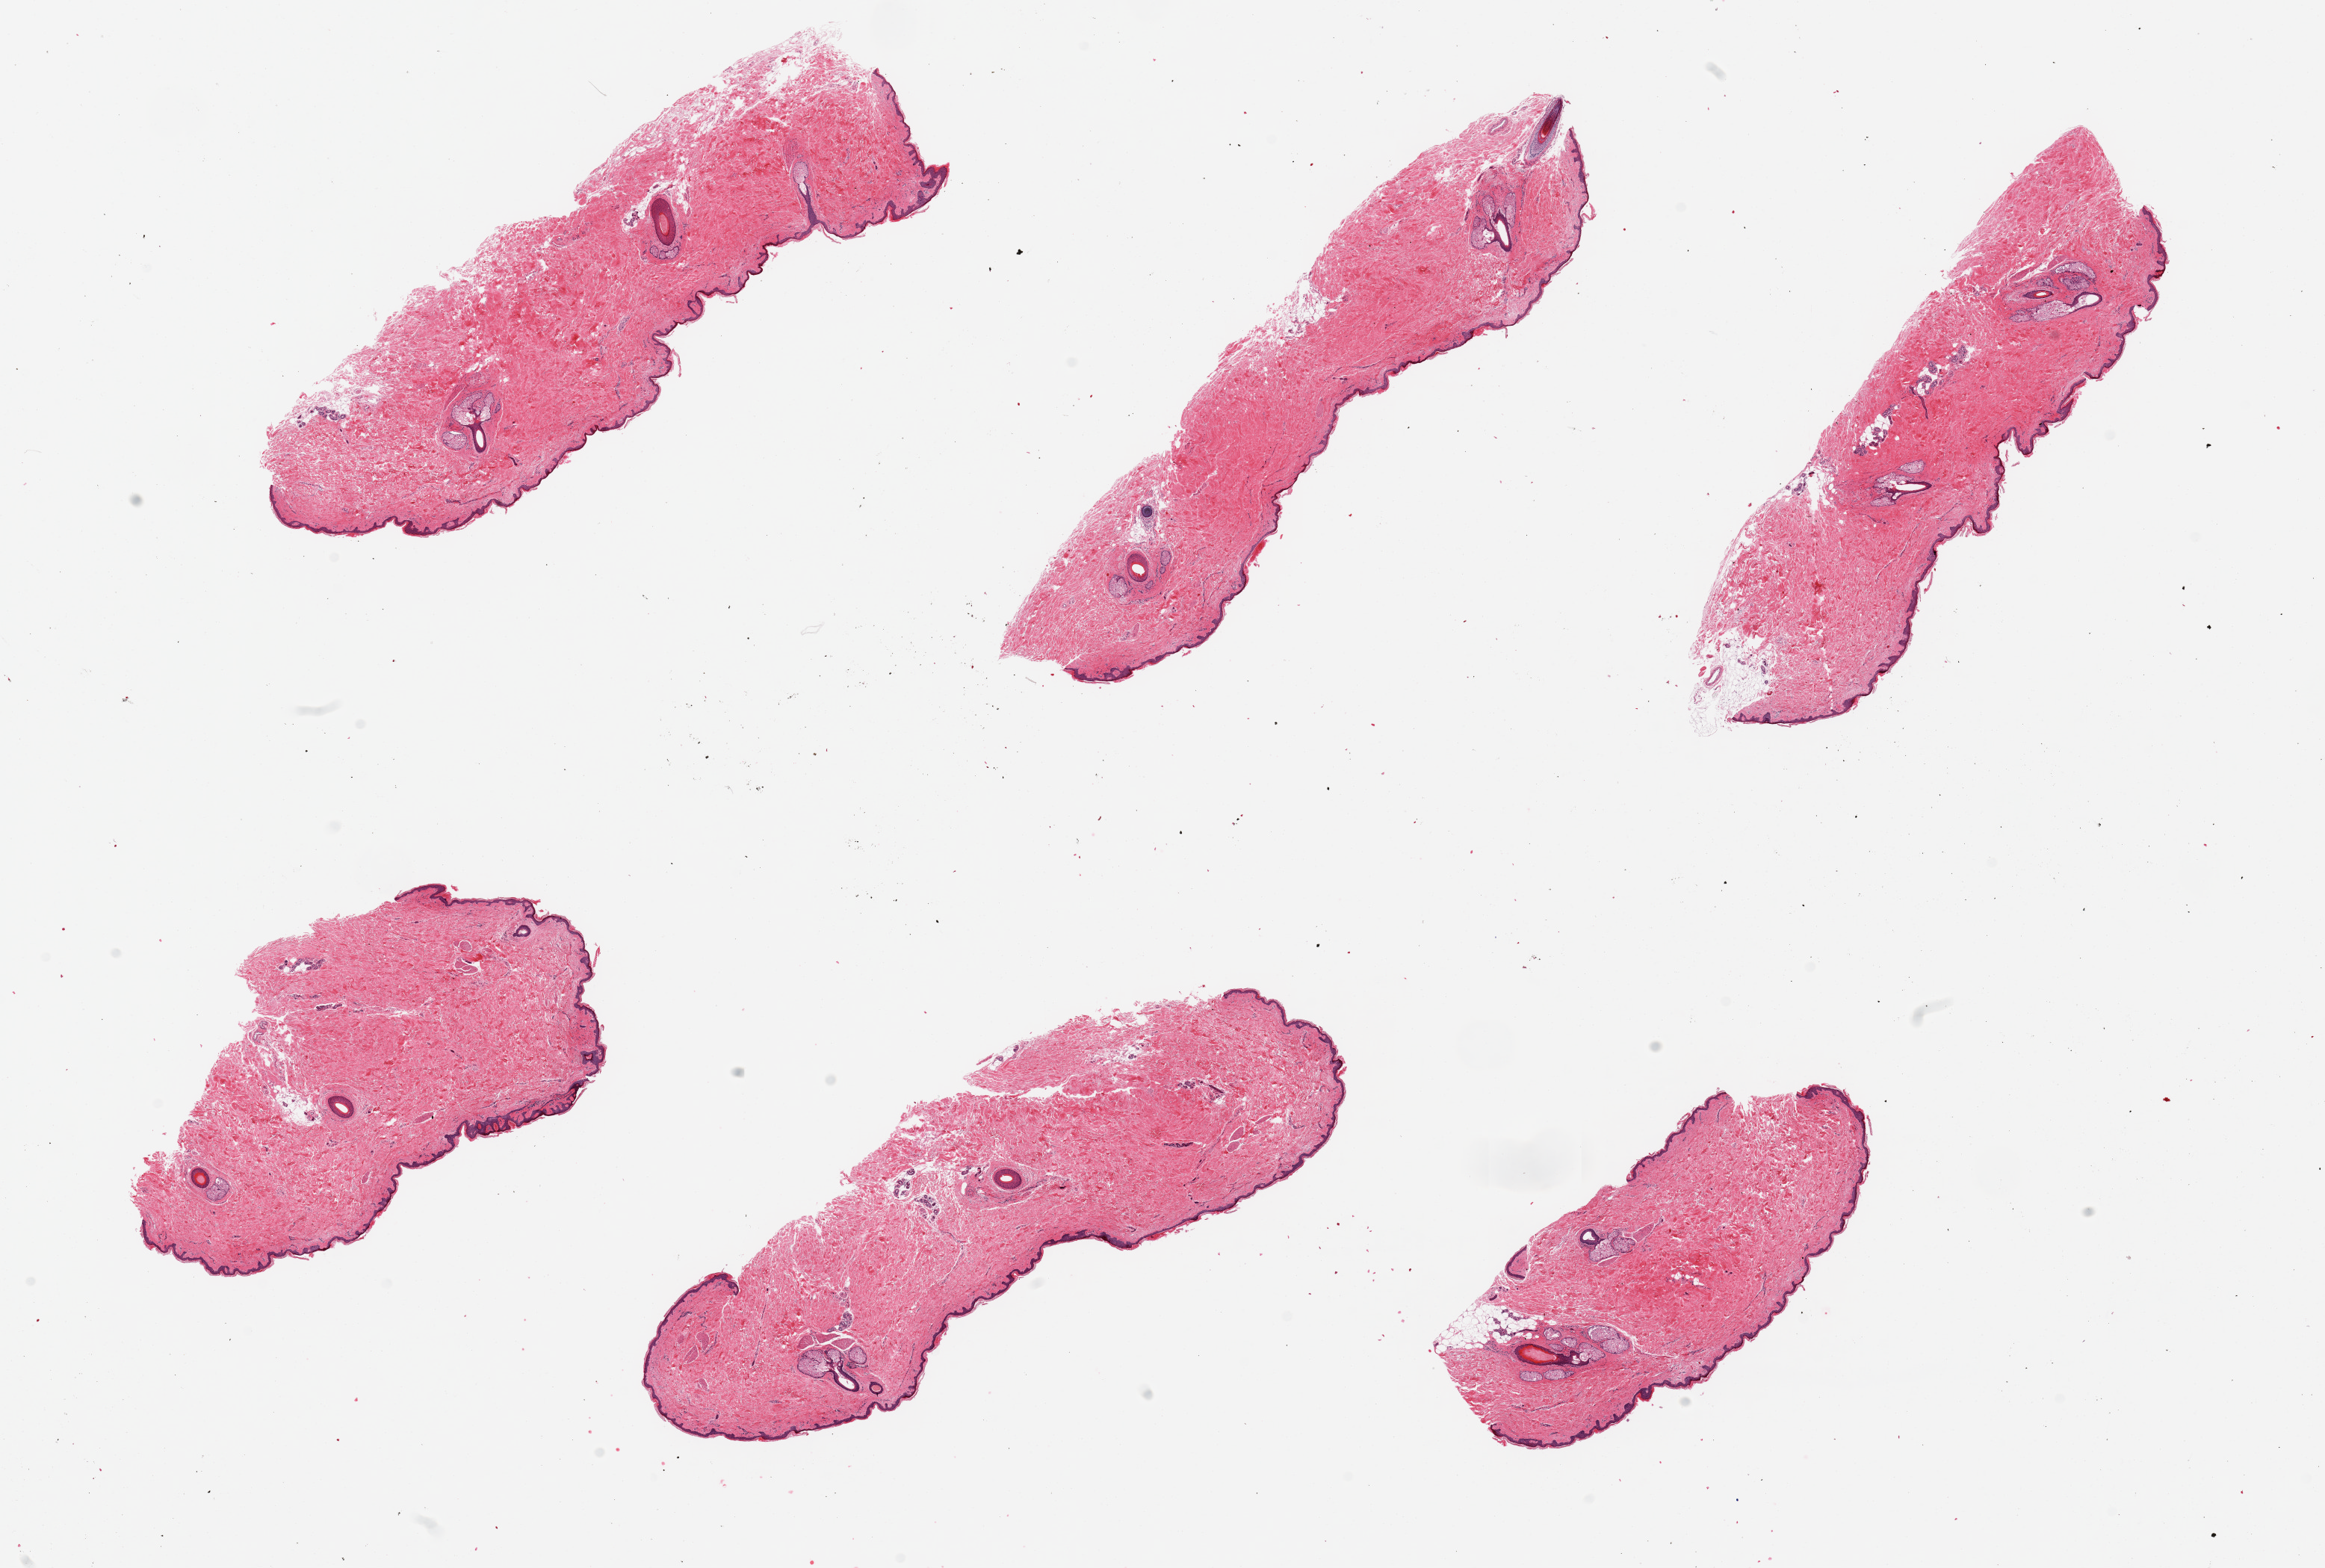
Digitized H&E-stained section, shown as a low-resolution overview of the whole scanned area (about 24.6 x 16.6 mm, slide scanned at 20x). PAXgene-fixed paraffin-embedded (PFPE) section. Target tissue: skin of suprapubic region. Donor tissue sample.
Pathologist's review note for this sample: 6 pieces; at least 2 hair follicles in each piece; well trimmed; 5% intradermal fat.